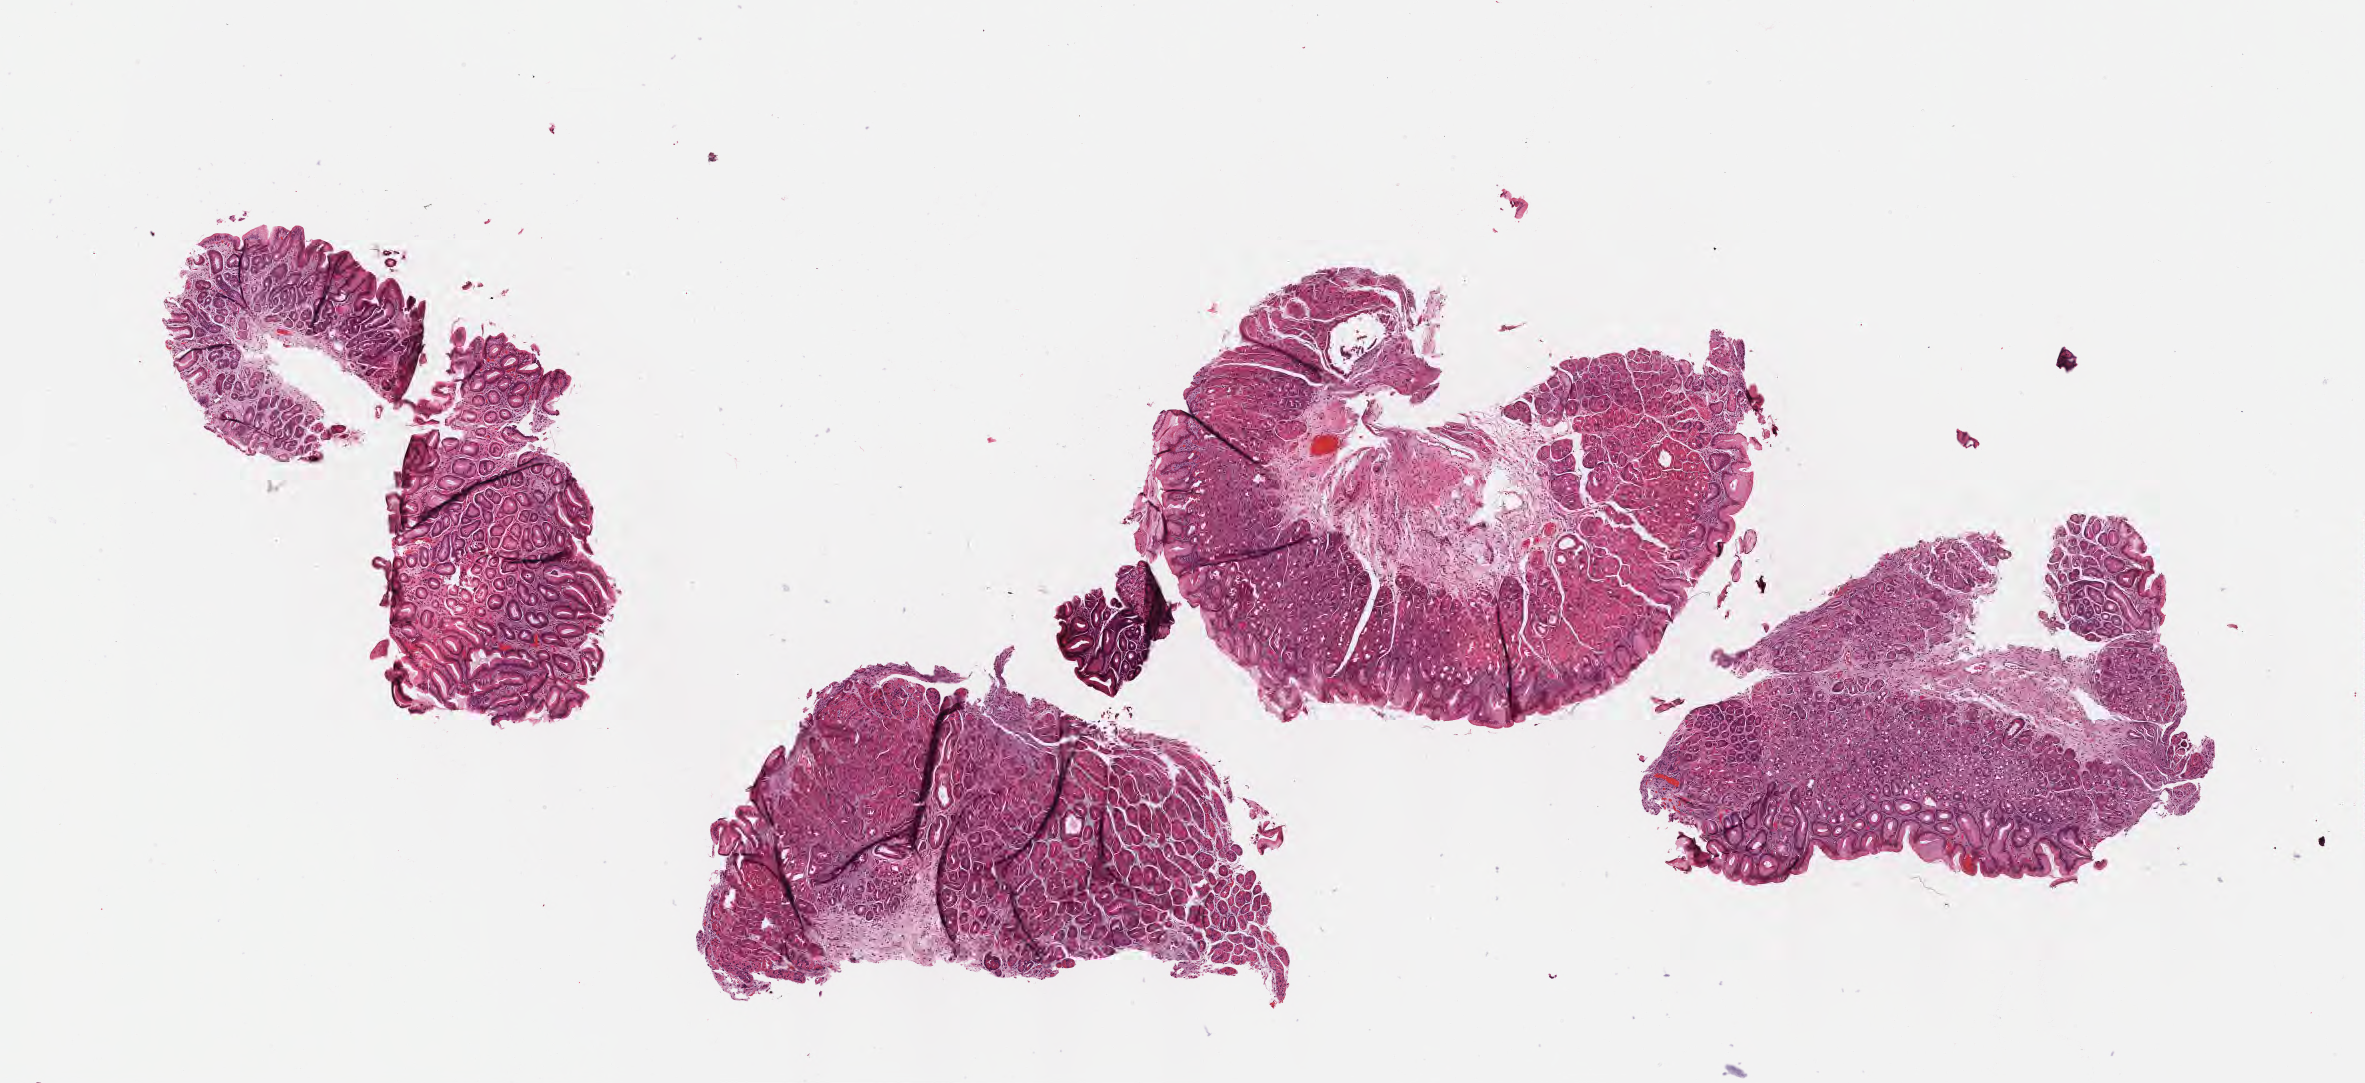
Digitized hematoxylin and eosin (H&E)-stained section — whole scanned area (about 9.6 x 4.4 mm) shown as a low-resolution overview. Formalin-fixed paraffin-embedded section. Normal-tissue sample (non-tumor) from a patient with burkitt lymphoma, NOS. Female patient, 74 years old. Pathologist review of this section (percent, as recorded): tumor cells 0%, tumor nuclei 0%, stromal cells 0%, necrosis 0%, normal cells 100%. Infiltration values recorded for this section: lymphocyte infiltration 20%, monocyte infiltration 5%, neutrophil infiltration 25%.
This section: non-tumor tissue sample; the patient's diagnosis is given above. Section: top of the tissue portion.